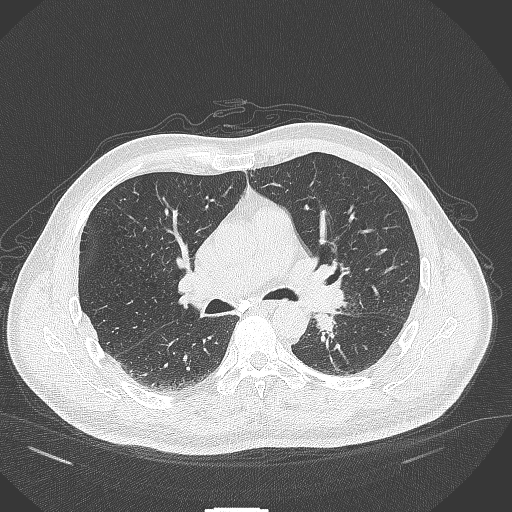
Chest CT, one axial slice; position 246 of 429 along the scan axis; reconstruction kernel B70f; 120 kVp; lung window (W 1500 / L -600 HU); 1 mm slice thickness; 512 × 512 image matrix, field of view 400 × 400 mm. Patient: male, 55 years. Case-level facts recorded for this patient, not image findings: clinical TNM (as recorded): T3 N0 M1c; histopathological grade: G3.
Outlined on this slice (rectangle marked by the reading radiologist):
- lung tumour (recorded histology: adenocarcinoma): bounding box <315,310,340,343> (left, top, right, bottom; pixels)